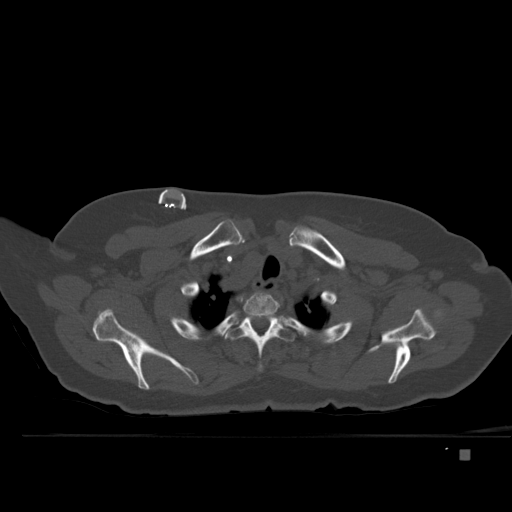
CT including the spine, one axial slice; position 395 of 477 along the scan axis; bone window (W 1800 / L 400 HU); 512 × 512 image matrix, field of view 422 × 422 mm. Female patient, age 74 years. From the clinical record (not read from this slice): primary cancer: colon.
Outlined on this slice (semi-automatic segmentation, software-assisted and operator-edited):
- T1 vertebra: box from (x=227, y=293) to (x=279, y=325) px
- T2 vertebra: (x=219, y=313)–(x=307, y=372)